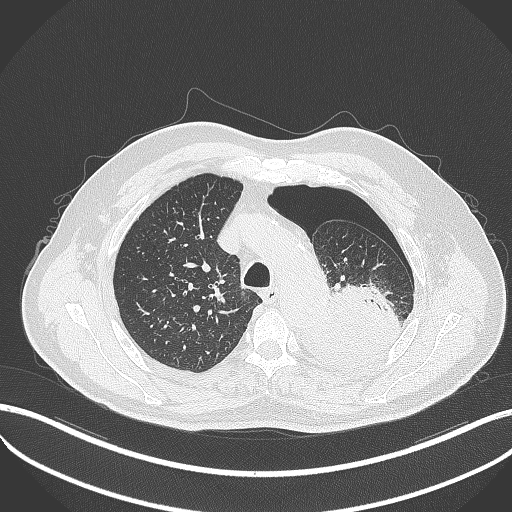
Chest CT, one axial slice. Position 384 of 464 along the scan axis. 120 kVp. Lung window (W 1500 / L -600 HU). 1 mm slice thickness. 512 × 512 image matrix. Patient: male, 76 years. From the clinical record (not read from this slice): clinical TNM (as recorded): T3 N0 M1b.
Annotated regions visible in this slice (bounding box drawn by a radiologist):
- lung tumour (recorded histology: adenocarcinoma): bounding box [x1, y1, x2, y2] px = [289, 285, 402, 374]